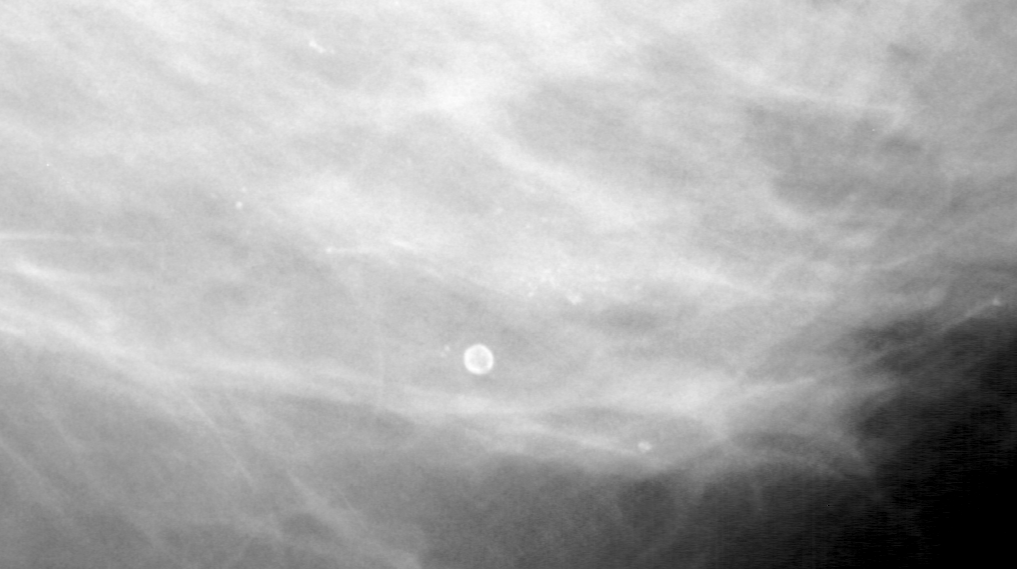
Cropped region of a digitized screen-film mammogram centred on a radiologist-marked abnormality; right breast; MLO view.
- Calcifications, morphology pleomorphic, distribution linear; BI-RADS assessment category 4; subtlety rating 3 on a 1 (subtle) to 5 (obvious) scale; pathology result (as recorded, not read from the image): benign.